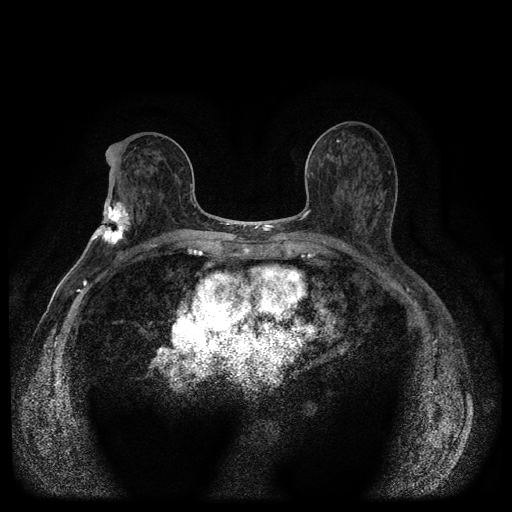
Breast MRI (dynamic contrast-enhanced, multi-phase), one axial slice. Position 55 of 116 along the scan axis. Dynamic contrast-enhanced series, time point 2 of 5 at this slice position (early post-contrast). 1.5 T. TE 2.7 ms, TR 5.4 ms. 2 mm slice thickness. 512 × 512 image matrix. Patient: female, 75 years.
Outlined on this slice (semi-automatic segmentation, software-assisted and operator-edited):
- breast lesion (labelled 'tumour' in the annotation; benign lesions carry a separate 'benign' label): box from (x=91, y=198) to (x=133, y=247) px